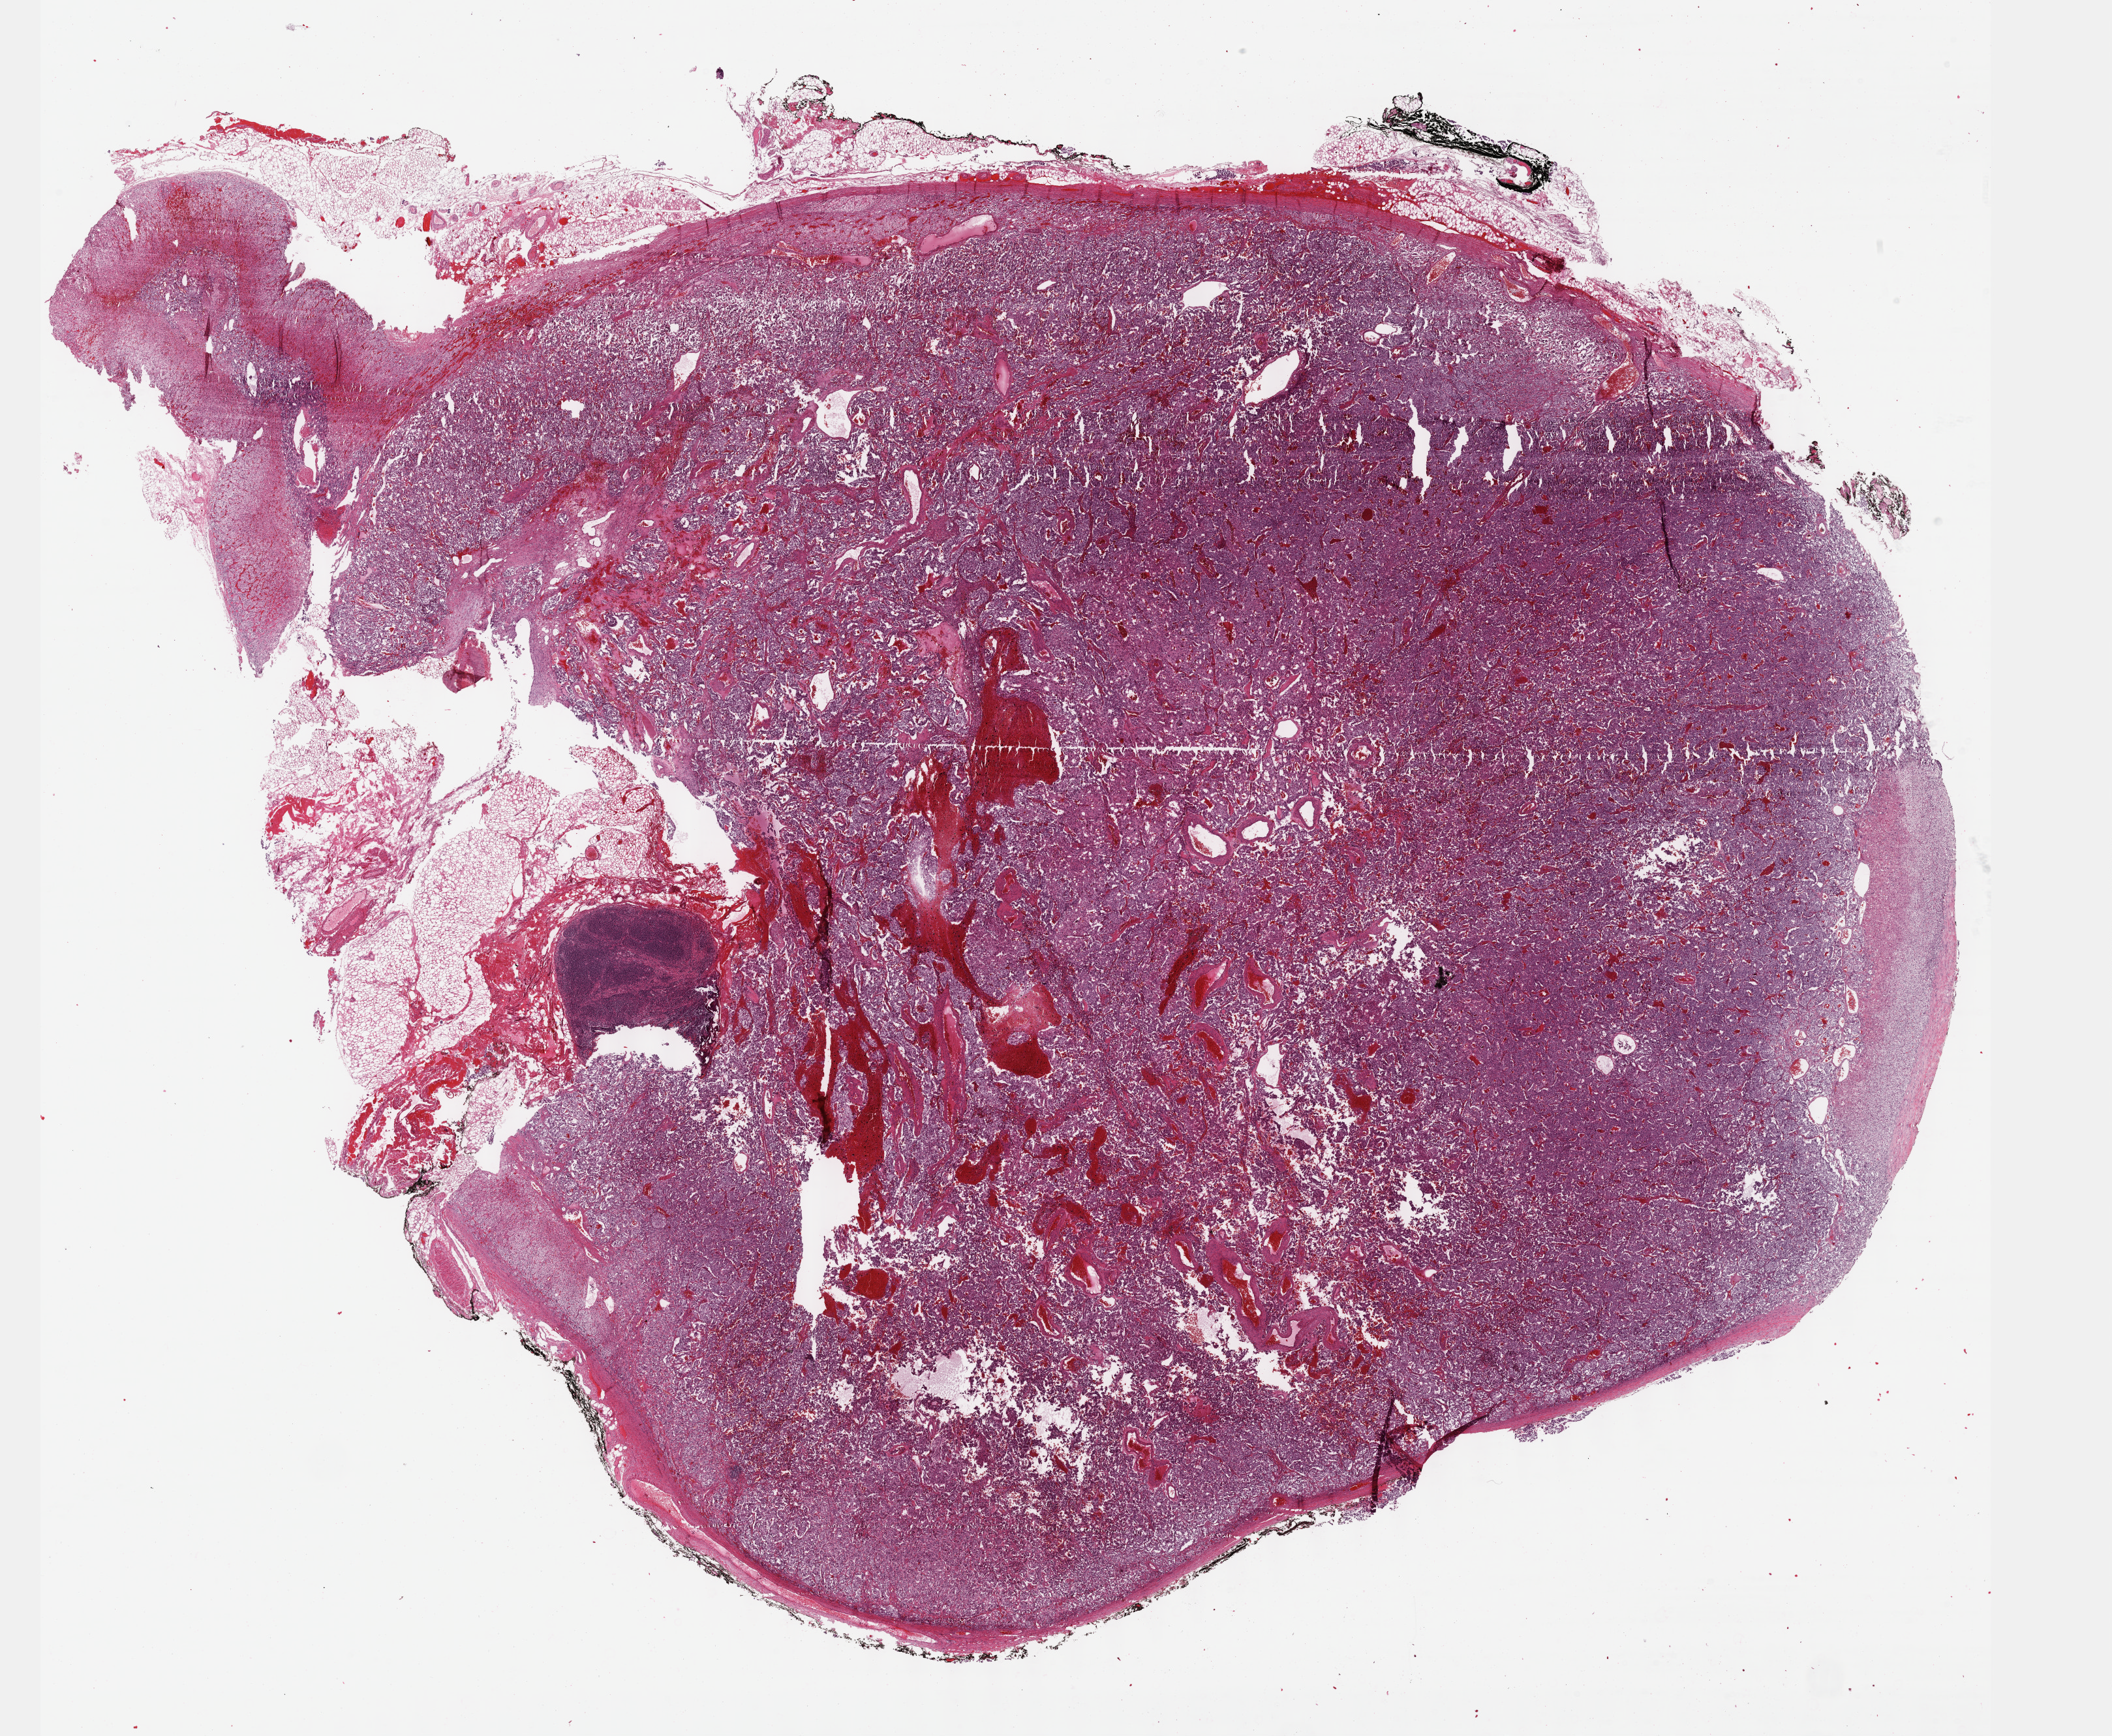
Whole-slide histology image, Hematoxylin and eosin (H&E) stained — a low-resolution overview of the entire scanned area, about 26.2 x 21.5 mm (acquisition: 40x scan), FFPE section, primary tumour sample from the adrenal gland. Female, age 30 years at initial diagnosis.
- pathologic diagnosis: Pheochromocytoma, NOS